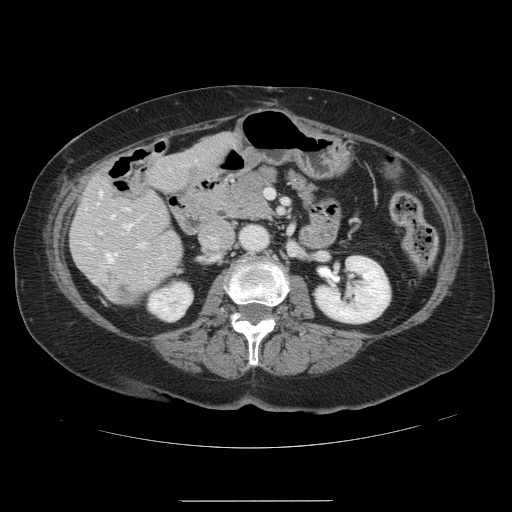
Contrast-enhanced abdominal CT, one axial slice. Position 48 of 141 along the scan axis. Intravenous contrast given. Soft-tissue window (W 400 / L 40 HU). 2.5 mm slice thickness. 512 × 512 image matrix, field of view 393 × 393 mm. Female patient, age 74 years. Case-level facts recorded for this patient, not image findings: diagnosis: colorectal cancer liver metastases, imaged before liver resection; multiple liver metastases: yes; largest metastasis: 7 cm; disease in both lobes: yes.
Structures marked on this image (outlined manually by an expert reader):
- hepatic veins: bounding box <99,191,130,262> (left, top, right, bottom; pixels)
- liver: <71,134,234,306>
- planned liver remnant (the part of the liver to remain after resection): <71,134,234,306>
- portal vein (with intrahepatic branches): <99,208,145,246>
- liver metastasis: <122,289,129,294>